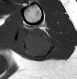
MRI of an extremity soft-tissue mass, one axial slice; slice 10 of 28 in the series (ordered by position); MR volume resampled by the dataset authors to the PET/CT grid (not the native acquisition matrix); 3.27 mm slice thickness; 77 × 79 image matrix, field of view 75 × 77 mm. Female patient. Case-level facts recorded for this patient, not image findings: histological type: malignant fibrous histiocytoma; grade: low; site of the primary tumour: left arm.
Outlined on this slice (expert contour drawn on MRI and transferred to this co-registered scan by the dataset authors):
- gross tumour volume (mass): bounding box (x1, y1, x2, y2) in pixels: (21, 29, 57, 60)